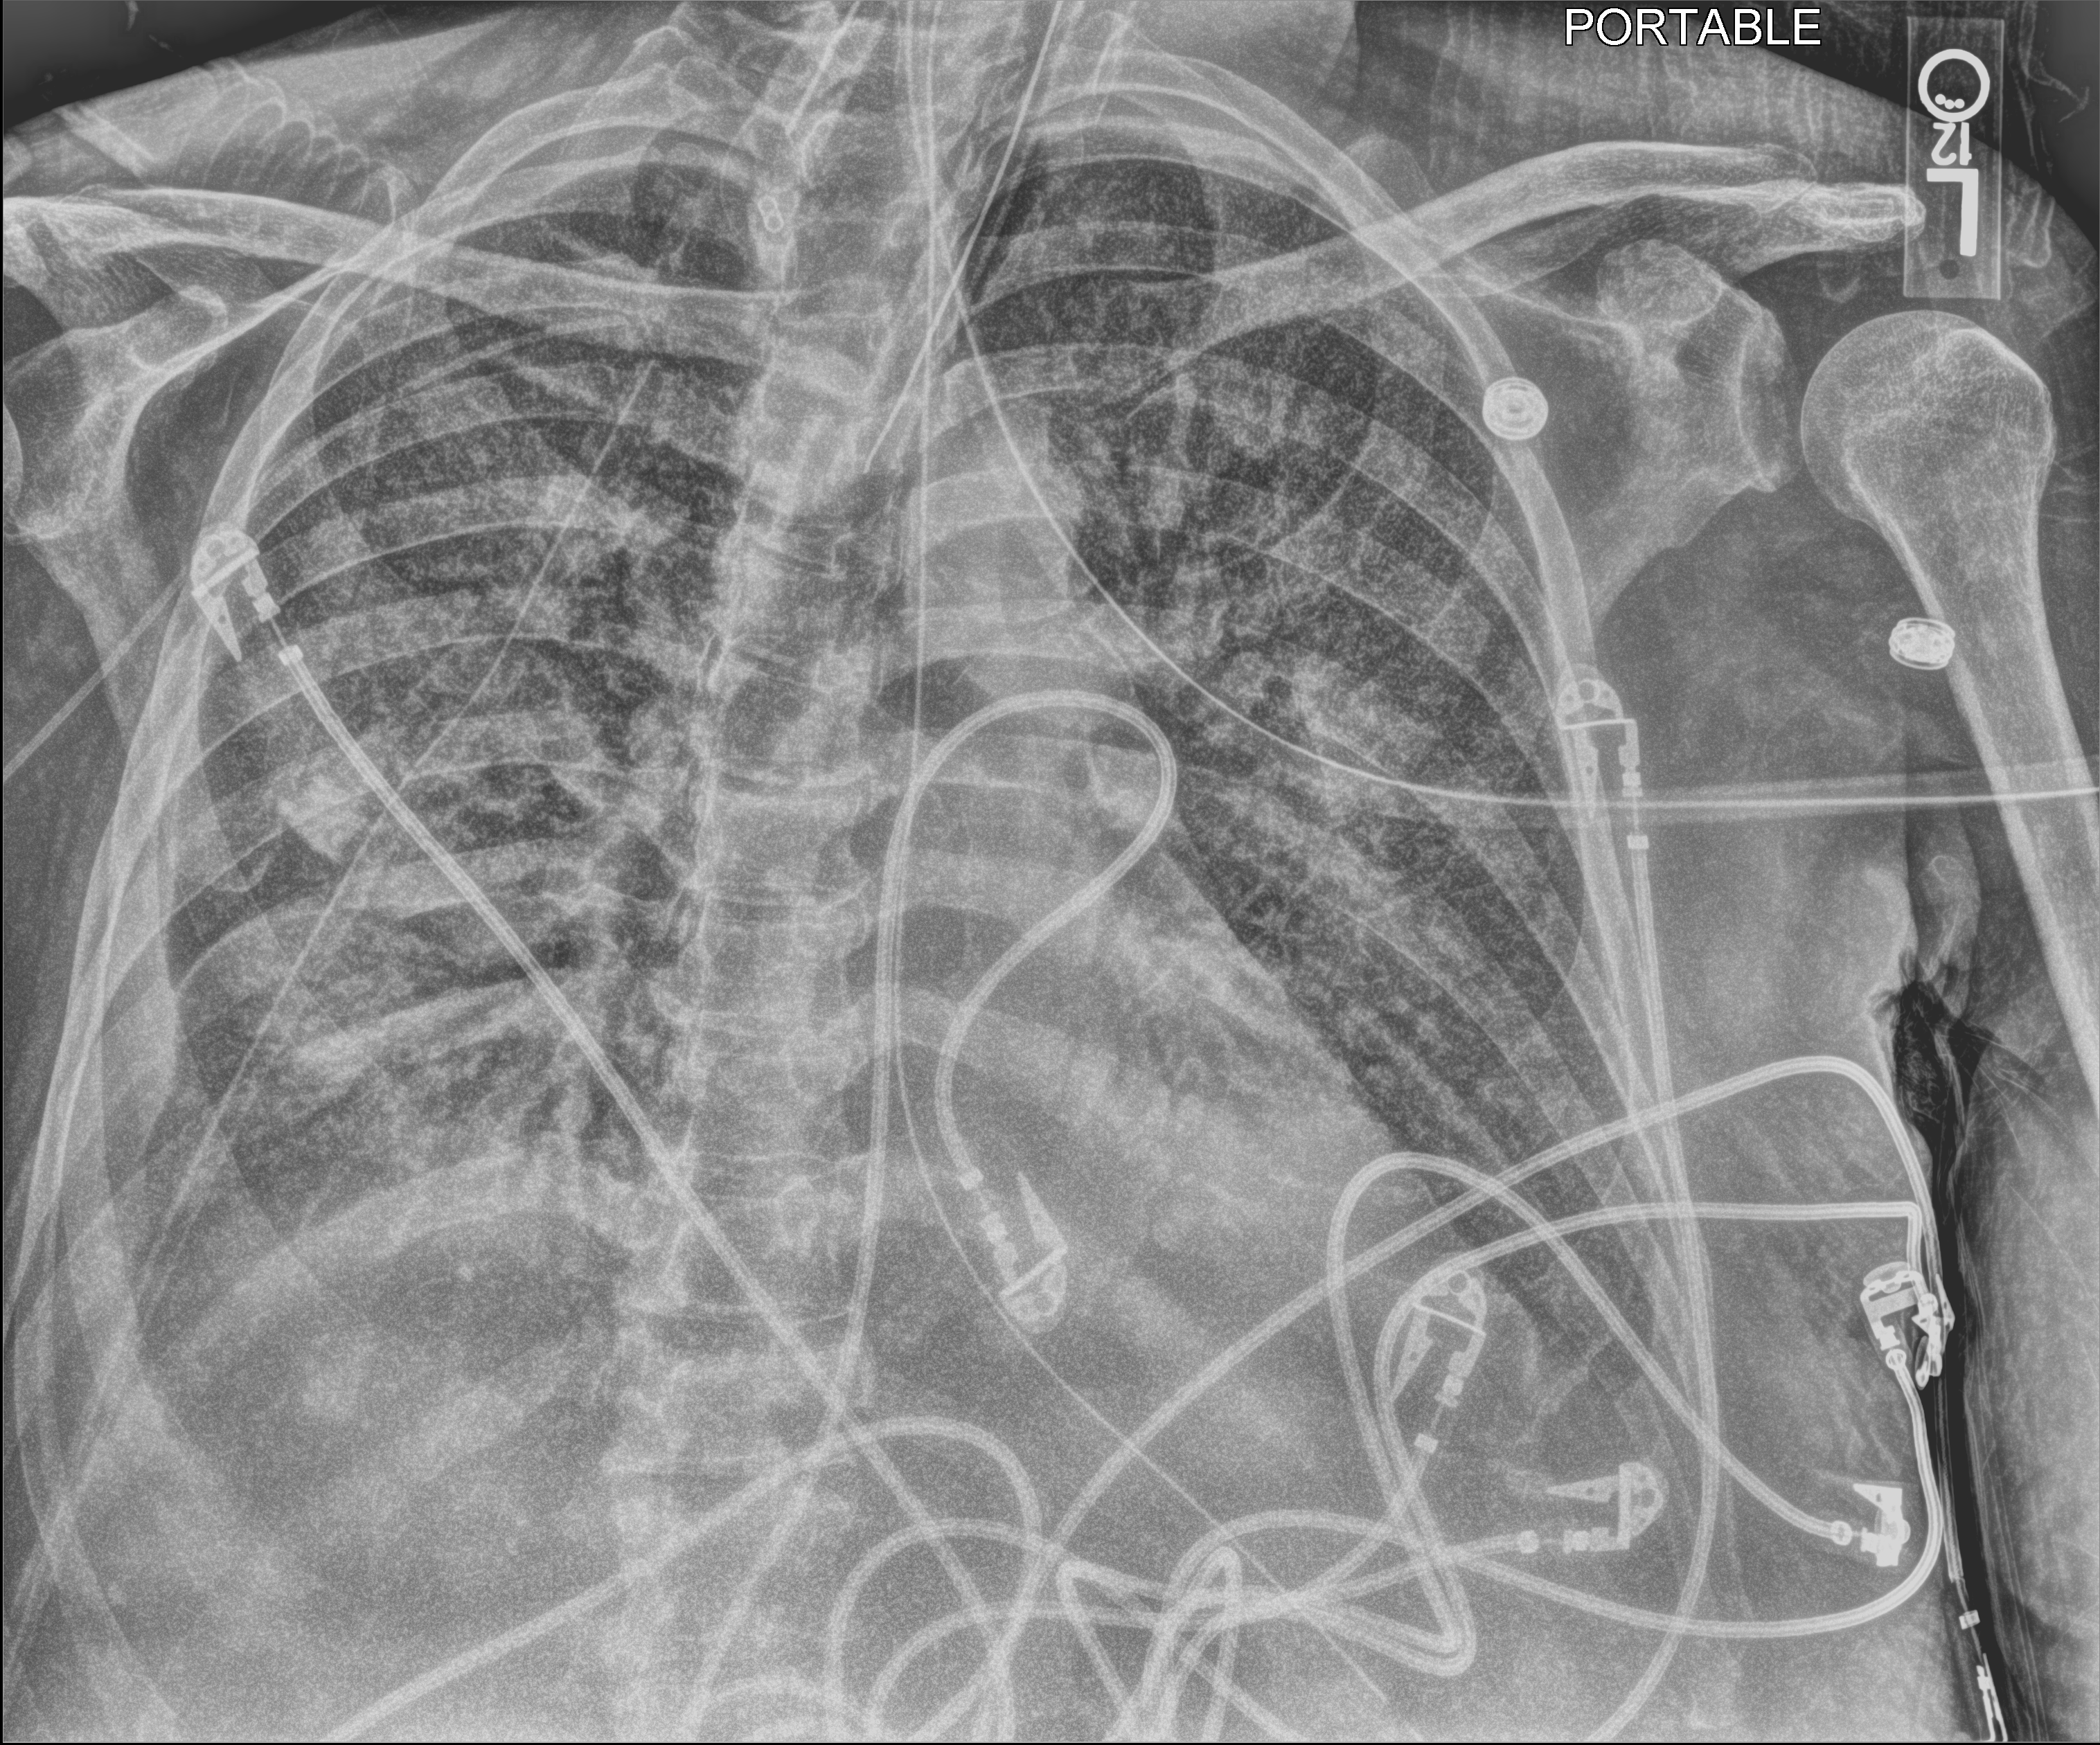
Chest X-ray (portable), anteroposterior (AP) projection. Male patient hospitalised with COVID-19, age 60–74 years.
Admission-level facts for this patient (not findings on this image; timing relative to this image not recorded):
- hypertension (admission record): no